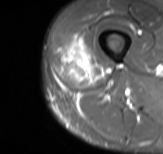
MRI of an extremity soft-tissue mass, one axial slice; position 21 of 61 along the scan axis; STIR; MR volume resampled by the dataset authors to the PET/CT grid (not the native acquisition matrix); 3.27 mm slice thickness; 163 × 154 image matrix. Male patient. Case-level facts recorded for this patient, not image findings: histological type: poorly differentiated synovial sarcoma; grade: high; site of the primary tumour: right buttock.
Annotated regions visible in this slice (expert contour drawn on MRI and transferred to this co-registered scan by the dataset authors):
- gross tumour volume including surrounding oedema: bounding box <59,36,106,86> (left, top, right, bottom; pixels)